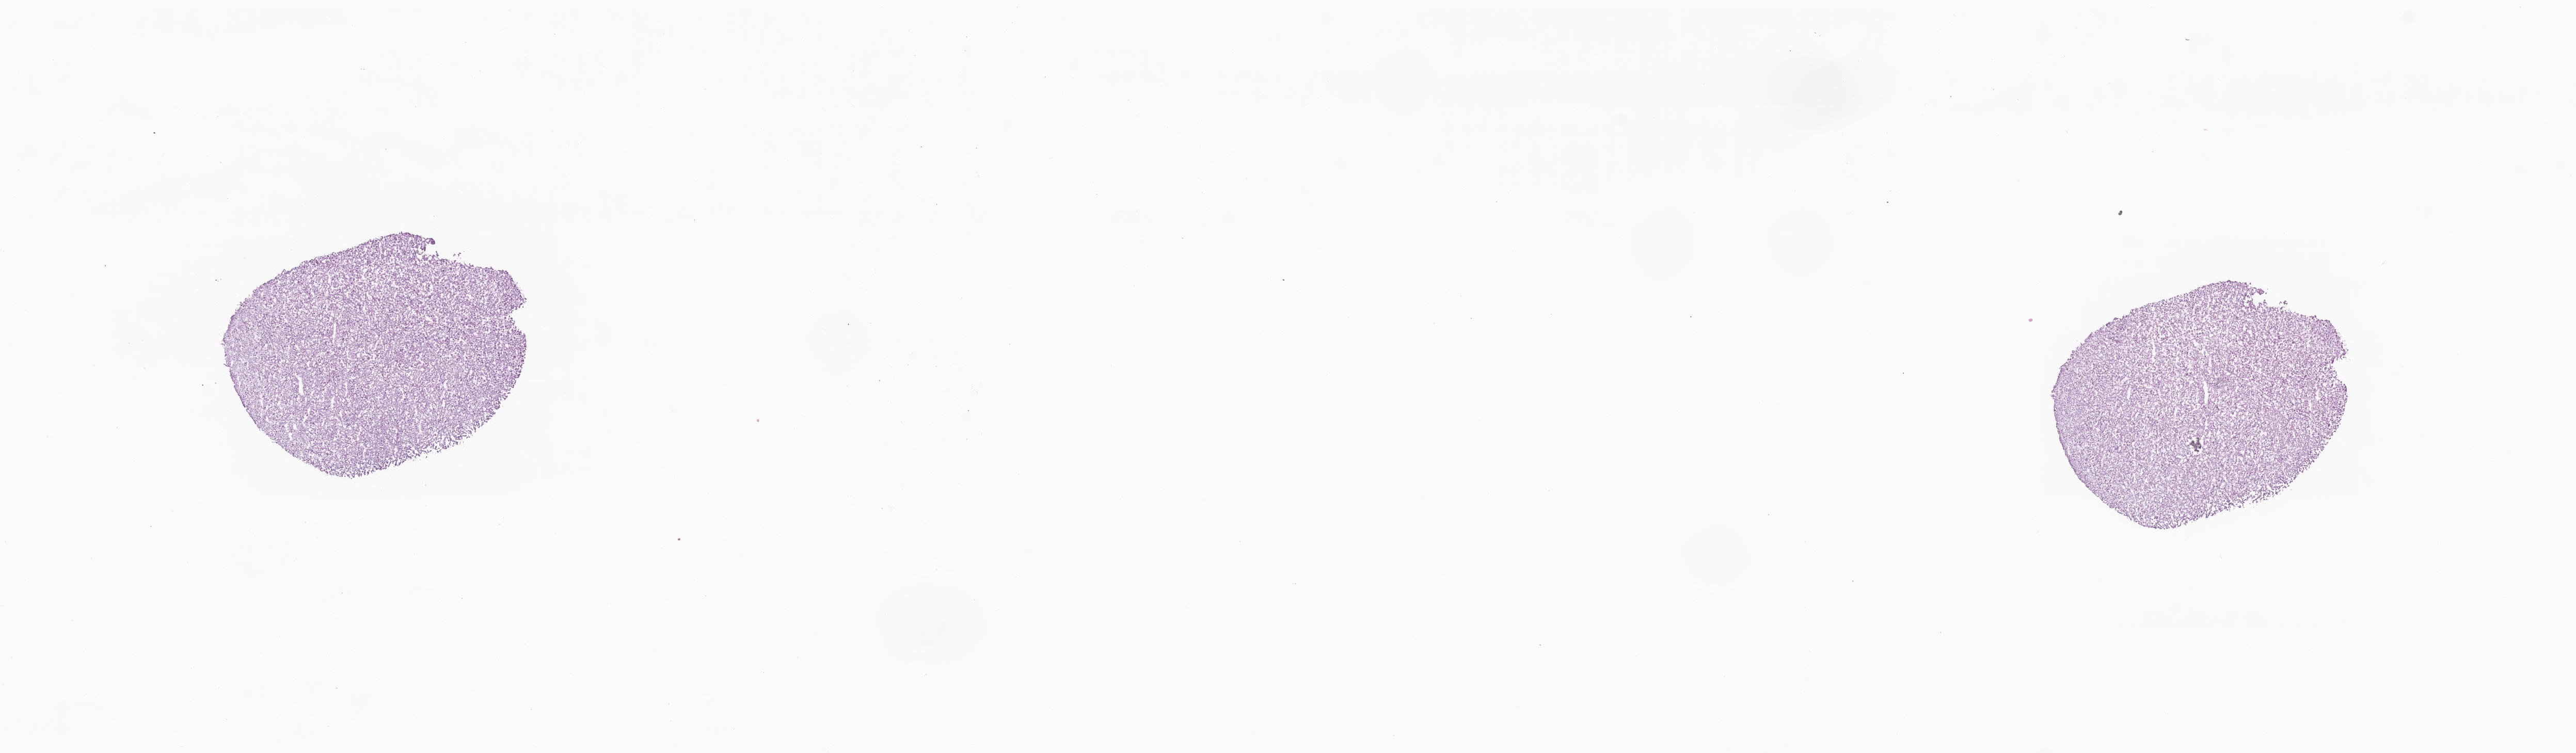
Whole-slide image, haematoxylin and eosin stain — low-resolution overview of the scanned area, about 21.0 x 6.1 mm, frozen section (tissue freezing medium), metastatic tumor tissue. Female, age 50 years at initial diagnosis. Slide review estimates, as recorded: tumor cells 95%, tumor nuclei 95%, stromal cells 5%, necrosis 0%, normal cells 0%. Inflammatory infiltration, as recorded: lymphocyte infiltration 0%, monocyte infiltration 0%, neutrophil infiltration 0%.
- patient diagnosis (primary): Adenocarcinoma, metastatic, NOS